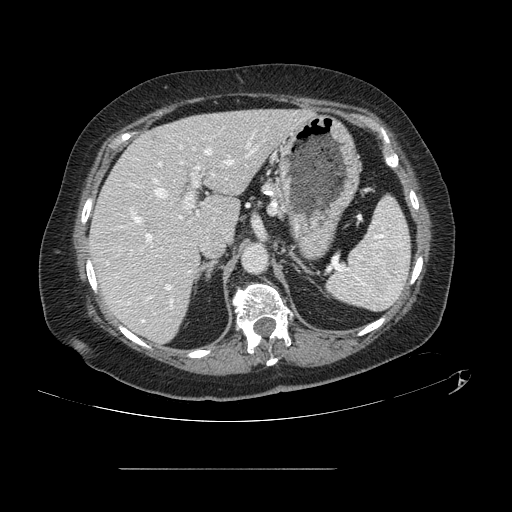
Contrast-enhanced abdominal CT, one axial slice; intravenous contrast given; soft-tissue window (W 400 / L 40 HU); 512 × 512 image matrix, field of view 439 × 439 mm. Female patient, age 75 years. From the clinical record (not read from this slice): diagnosis: colorectal cancer liver metastases, imaged before liver resection; multiple liver metastases: no; largest metastasis: 2.4 cm.
Structures marked on this image (outlined manually by an expert reader):
- hepatic veins: bounding box [x1, y1, x2, y2] px = [142, 150, 211, 323]
- liver: [90, 110, 309, 343]
- planned liver remnant (the part of the liver to remain after resection): [90, 110, 309, 343]
- portal vein (with intrahepatic branches): [131, 133, 259, 290]